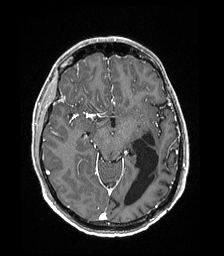
Brain MRI from a brain-tumour surgery series, one axial slice; position 107 of 192 along the scan axis; T1-weighted post-contrast; 224 × 256 image matrix, field of view 224 × 256 mm. From the clinical record (not read from this slice): histopathology: Low grade glioma; IDH mutation: no; tumour location: Left Parieto-Occipital Intraventricular.
Structures marked on this image (expert manual segmentation):
- previous resection cavity: bounding box <124,132,159,205> (left, top, right, bottom; pixels)